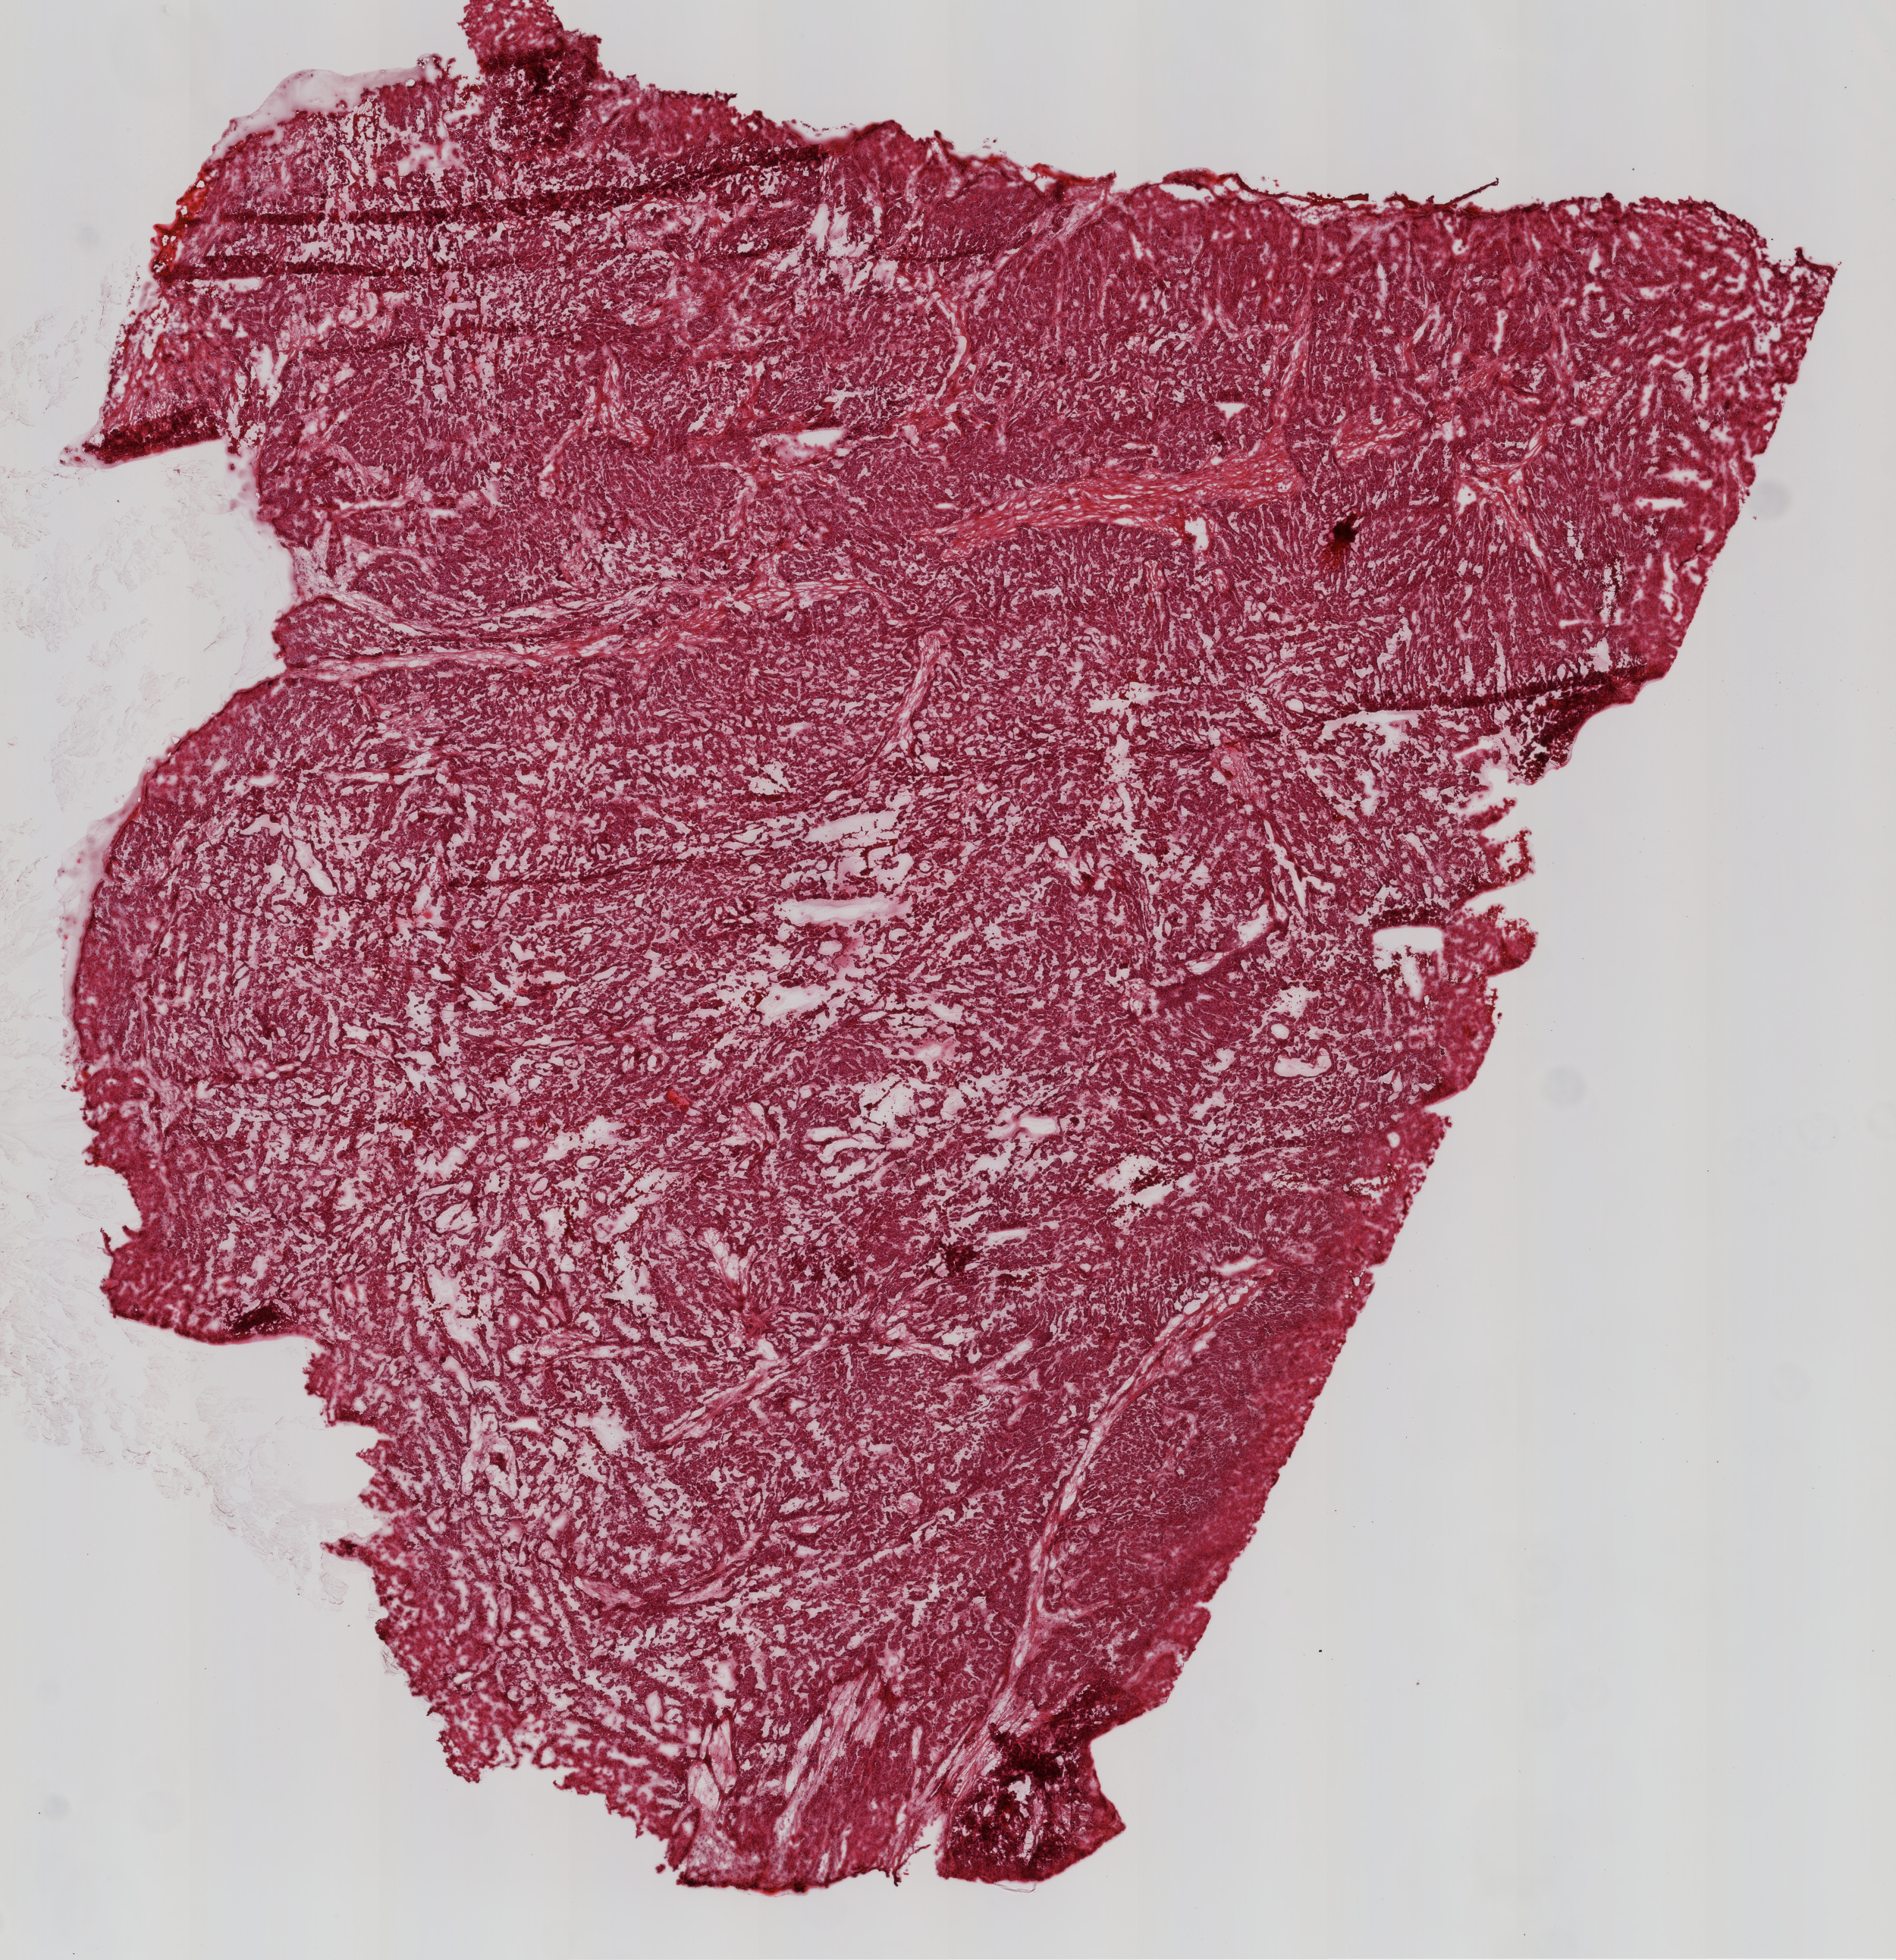
H&E whole-slide image — a low-resolution overview of the entire scanned area, about 10.0 x 10.4 mm (slide scanned at 20x). Frozen section. Primary tumour sample from the ovary. Female patient; age at initial diagnosis 77 years. Histologic grade: G3 (poorly differentiated). Pathologist review of this section (percent, as recorded): tumour cells 95%, tumour nuclei 99%, normal cells 0%, stromal cells 3%, necrosis 2%.
Laterality: left. Histologic diagnosis: Serous cystadenocarcinoma, NOS. FIGO stage: IIIC.